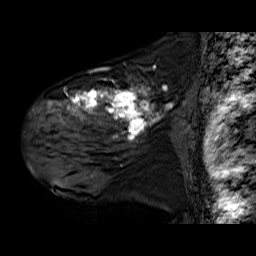
Breast MRI (dynamic contrast-enhanced), one sagittal slice. Slice 44 of 60 in the series (ordered by position). Dynamic contrast-enhanced series, time point 2 of 6 at this slice position (early post-contrast). 1.5 T. TE 6.3 ms, TR 32.9 ms. 256 × 256 image matrix, field of view 200 × 200 mm. Female patient. From the clinical record (not read from this slice): setting: breast cancer imaged before/during neoadjuvant chemotherapy; receptor status: HER2-positive.
Outlined on this slice (semi-automatically segmented with operator editing):
- analysis volume of interest (the breast-tissue region the enhancement analysis was run in; not a lesion): bounding box [x1, y1, x2, y2] px = [30, 78, 181, 180]
- tumour enhancement mask (voxels above the 100 % enhancement threshold inside the analysis volume of interest): [48, 86, 171, 177]